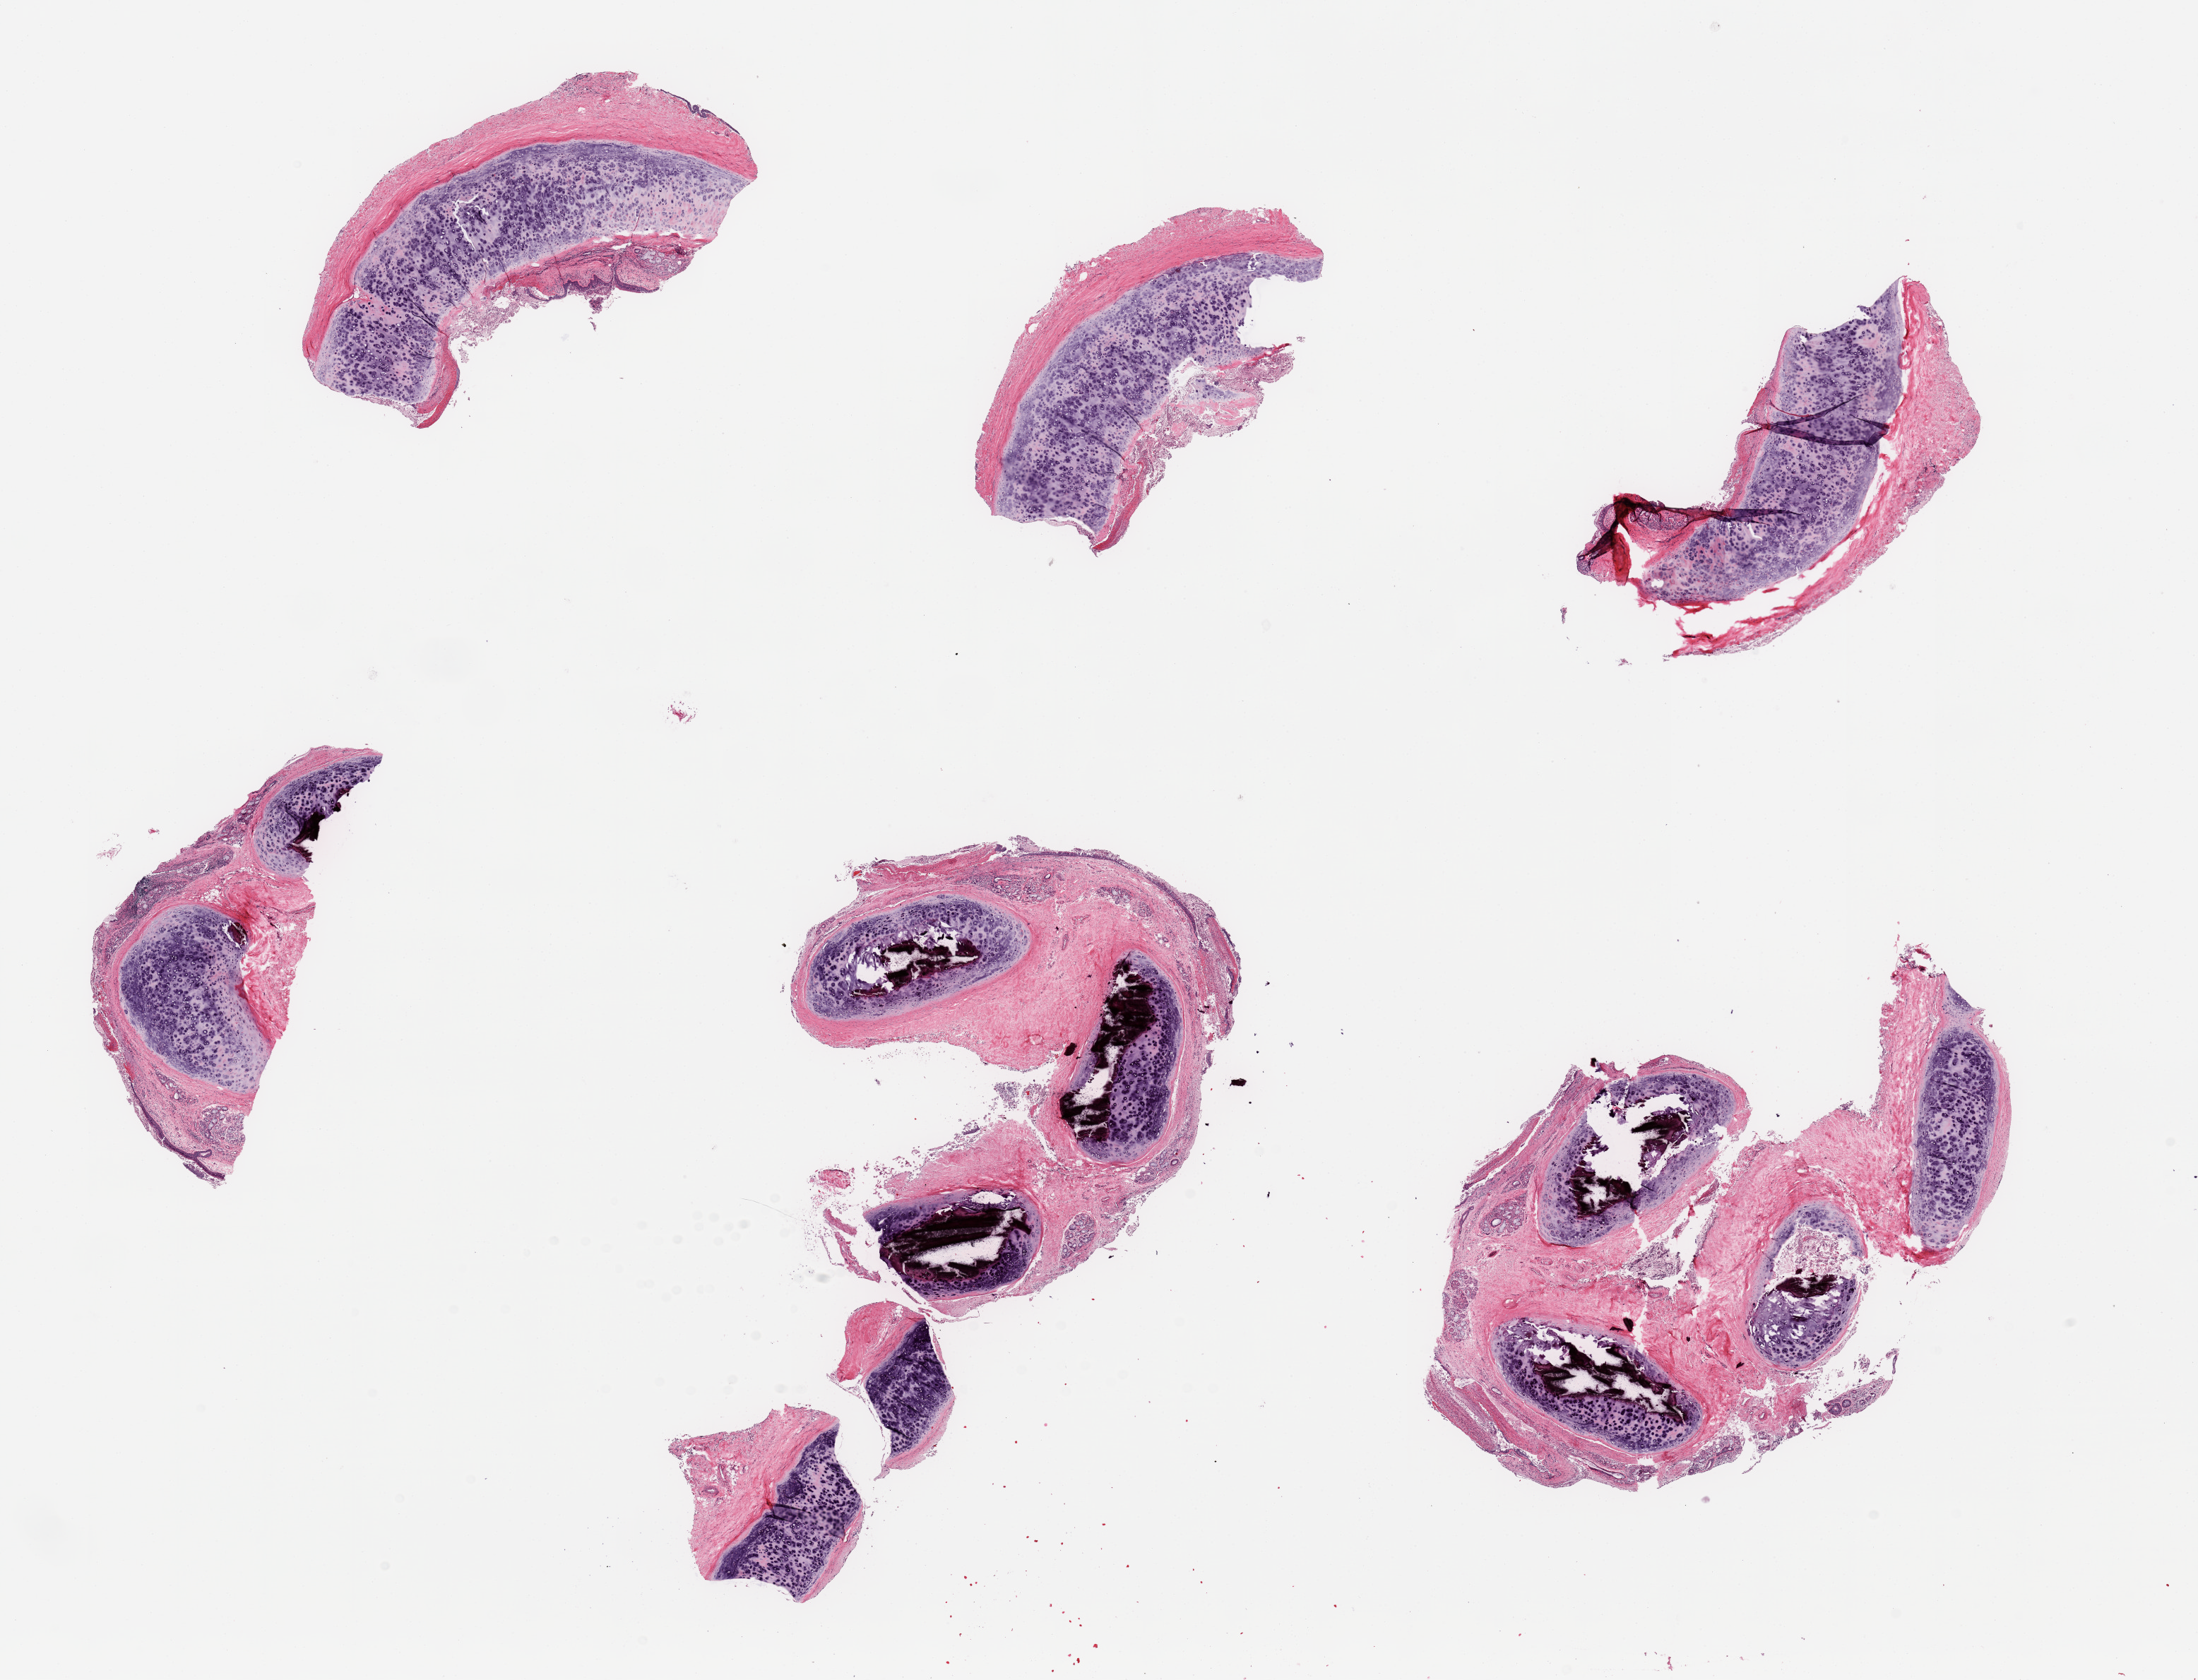
Whole-slide image, H&E stain, low-resolution overview of the scanned area, about 24.6 x 18.8 mm (acquisition: 20x scan), PAXgene-fixed paraffin-embedded (PFPE) section, target tissue: esophageal muscle, tissue donor sample. Donor sex: female.
Reviewer comment on this tissue sample: 6 pieces; trachea sampled.